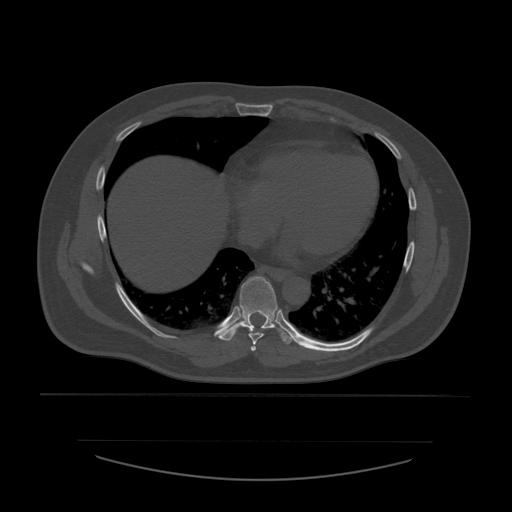
CT including the spine, one axial slice. Reconstruction kernel STANDARD. Bone window (W 1800 / L 400 HU). 1.25 mm slice thickness. 512 × 512 image matrix, field of view 441 × 441 mm. Patient age 44 years. Case-level facts recorded for this patient, not image findings: primary cancer: soft tissue sarcoma.
Structures marked on this image (semi-automatic segmentation, software-assisted and operator-edited):
- T6 vertebra: bounding box [x1, y1, x2, y2] px = [251, 346, 257, 353]
- T7 vertebra: [249, 332, 265, 345]
- T8 vertebra: [216, 276, 295, 345]